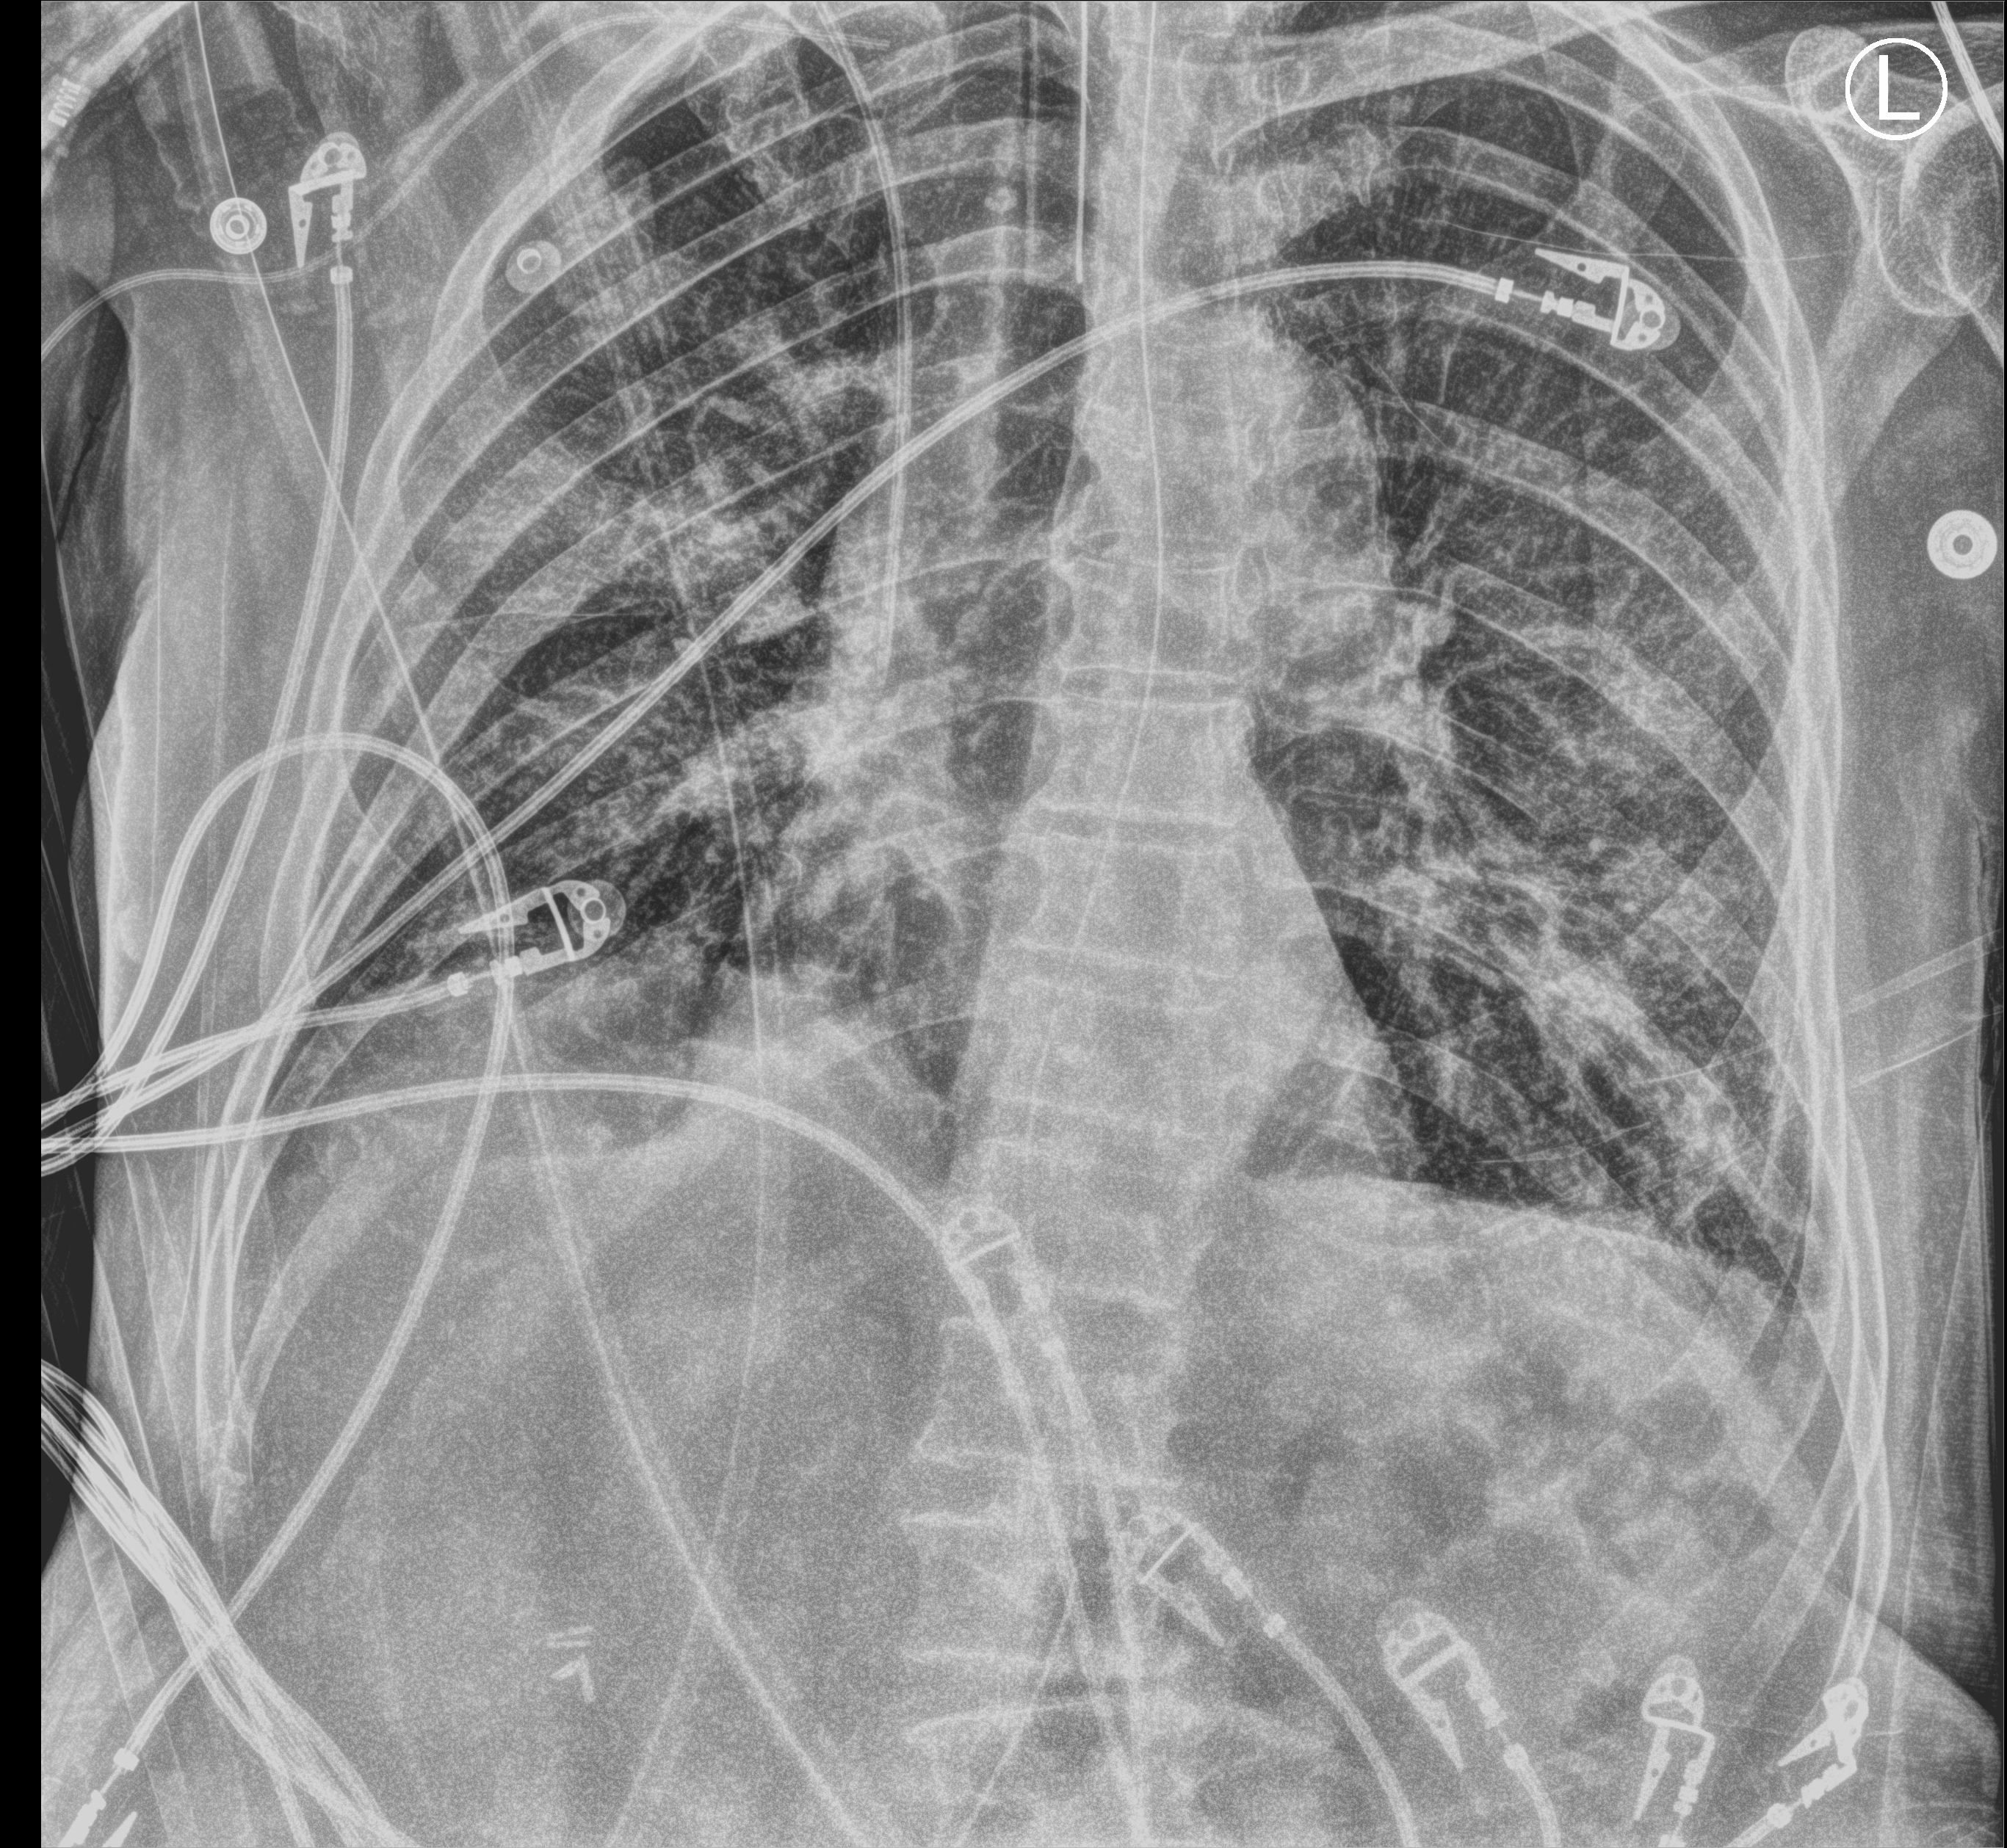
Bedside chest radiograph (computed radiography), anteroposterior (AP) projection. Patient hospitalised with COVID-19; male, aged 75–90 years.
Admission-level facts for this patient (not findings on this image; timing relative to this image not recorded):
- admitted to intensive care during this hospital stay: yes
- length of hospital stay: 70 days